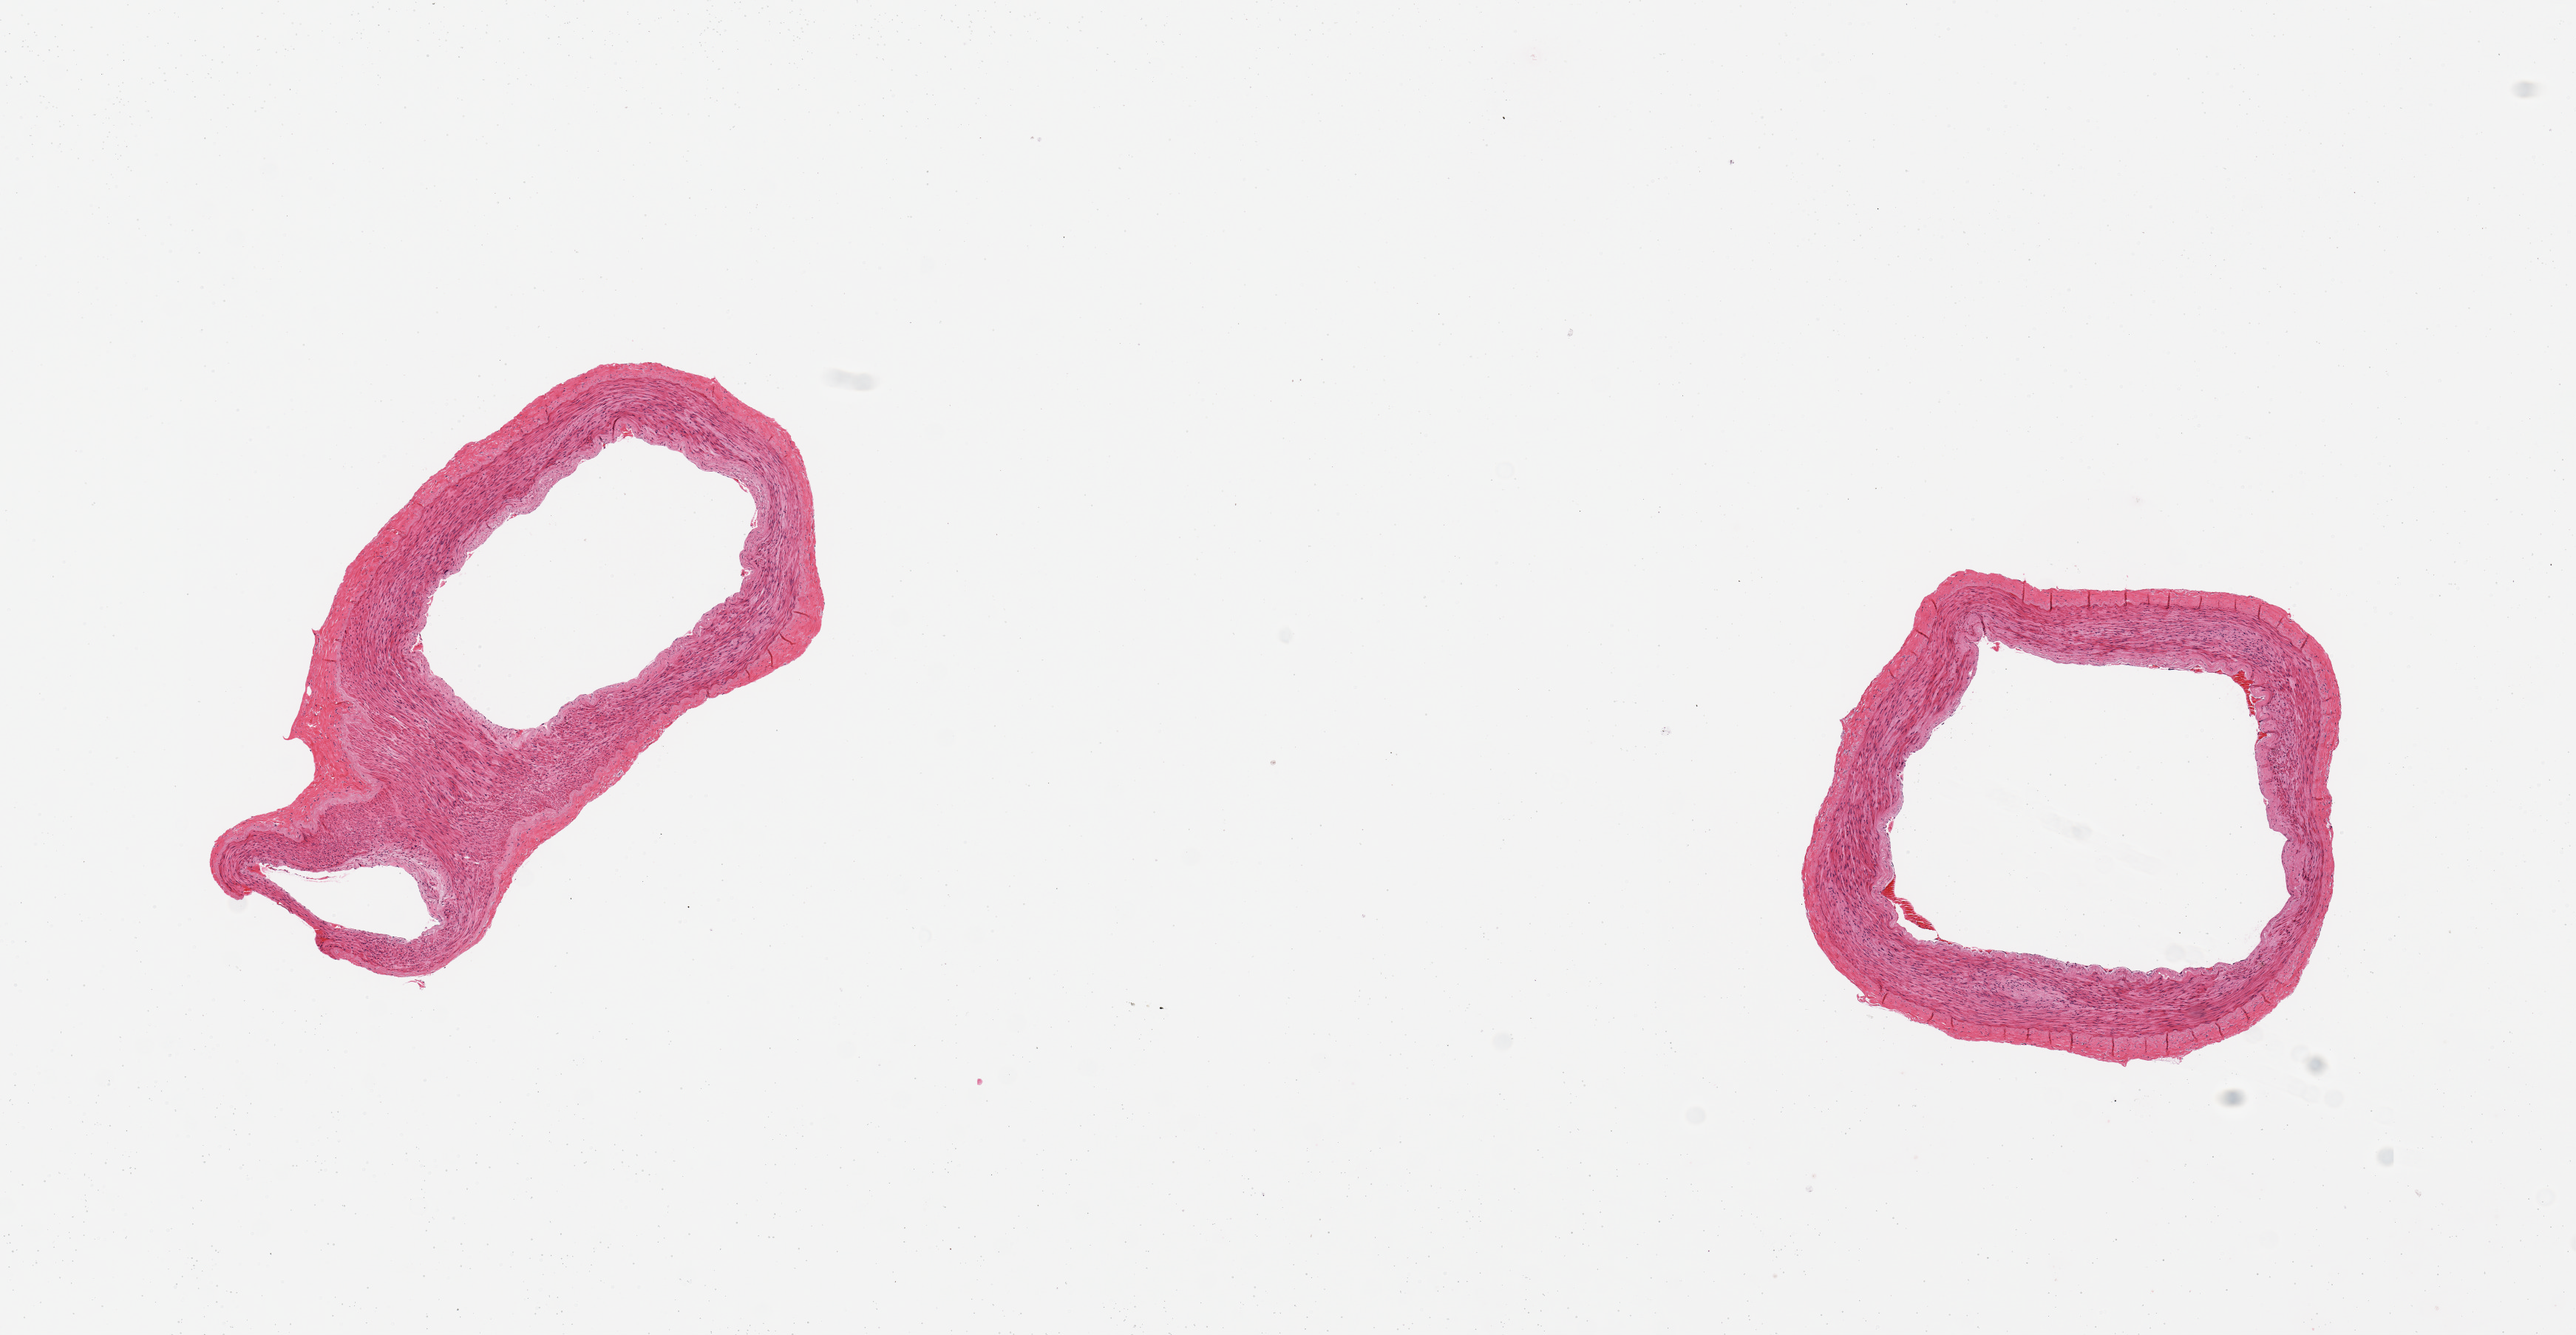
H&E whole-slide image — low-resolution overview of the scanned area, about 13.8 x 7.1 mm (slide scanned at 20x). PAXgene-fixed, paraffin-embedded tissue. Sampled site (target tissue): tibial artery. Donor tissue sample. Male donor.
Reviewer comment on this tissue sample: 2 pieces, no lesions.